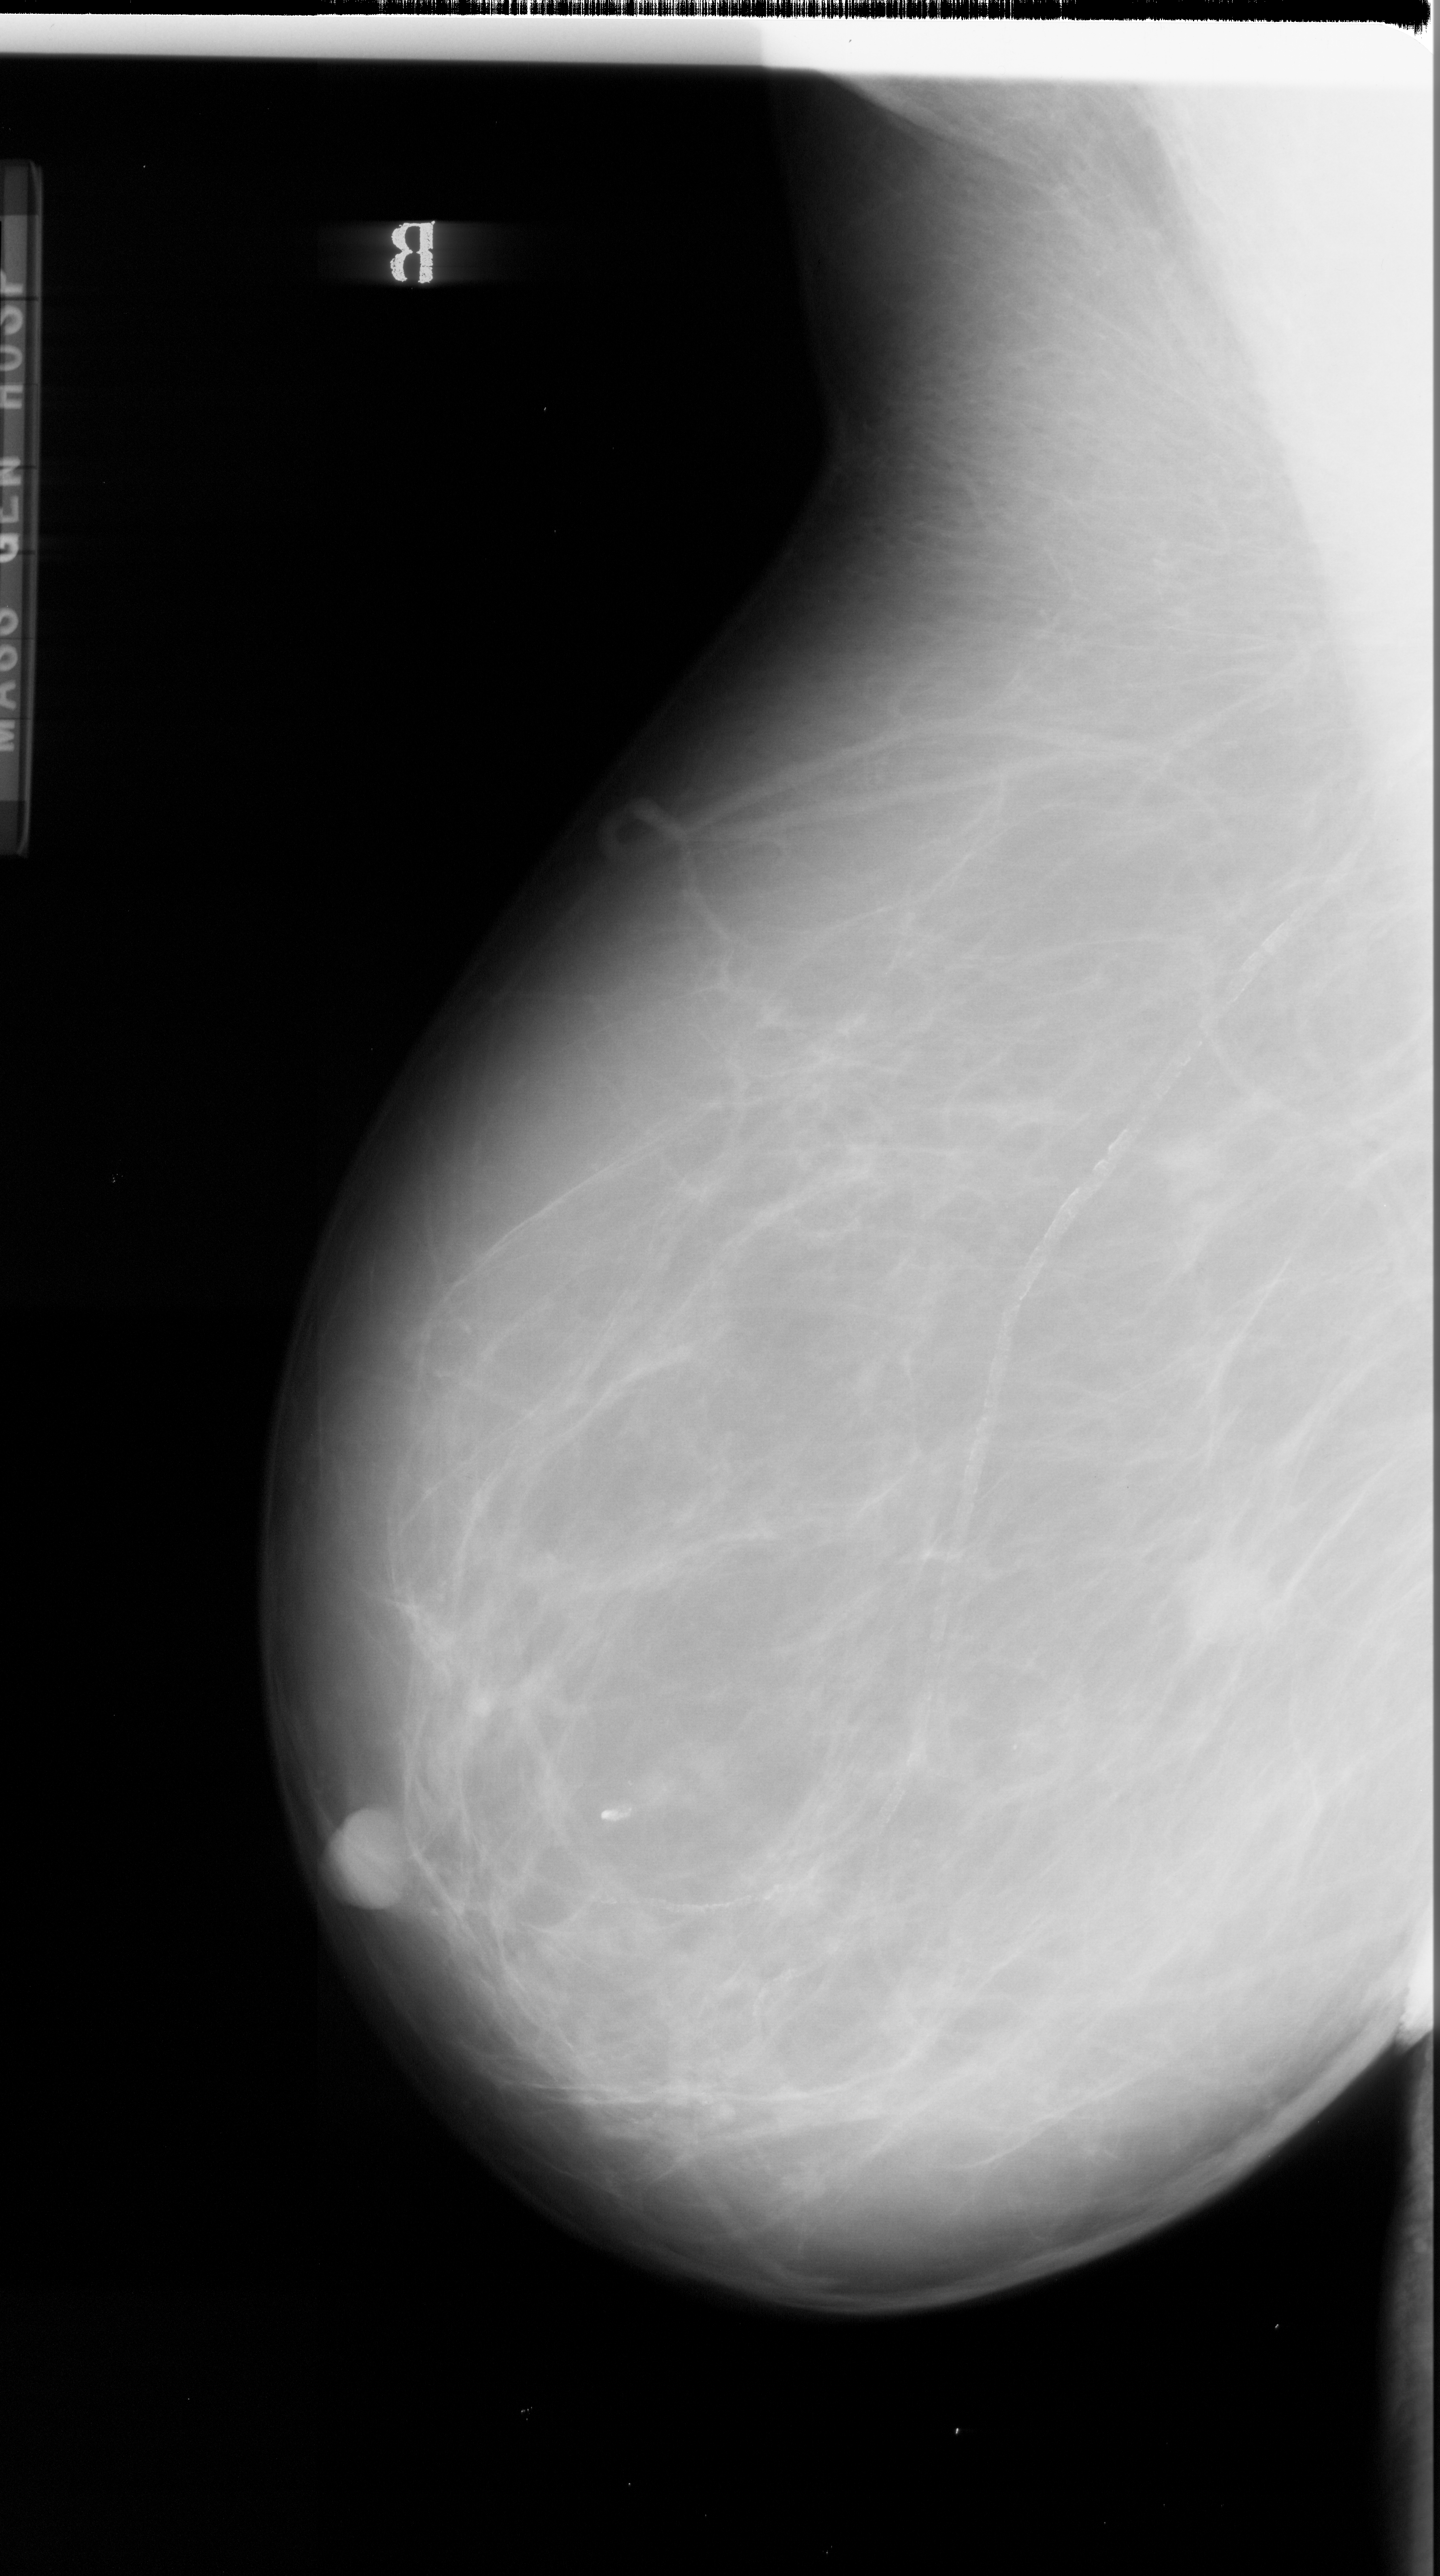
Digitized screen-film mammogram; left breast; mediolateral oblique (MLO) view; BI-RADS breast density category 1 (scale 1–4).
- Radiologist-marked abnormalities on this image: mass, shape irregular, margins spiculated; BI-RADS assessment category 5; subtlety rating 4 on a 1 (subtle) to 5 (obvious) scale; pathology (as recorded): malignant.